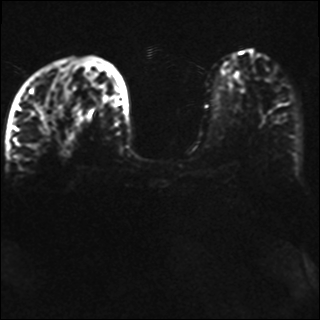
Breast MRI, one axial slice. Slice 15 of 42 in the series (ordered by position). Diffusion-weighted series; image 2 of 4 stored at this slice position (different b-values; order by instance number). 1.5 T. 4 mm slice thickness. 320 × 320 image matrix. Female patient.
Annotated regions visible in this slice (expert manual segmentation):
- tumour on diffusion-weighted imaging: bounding box (x1, y1, x2, y2) in pixels: (38, 107, 45, 122)